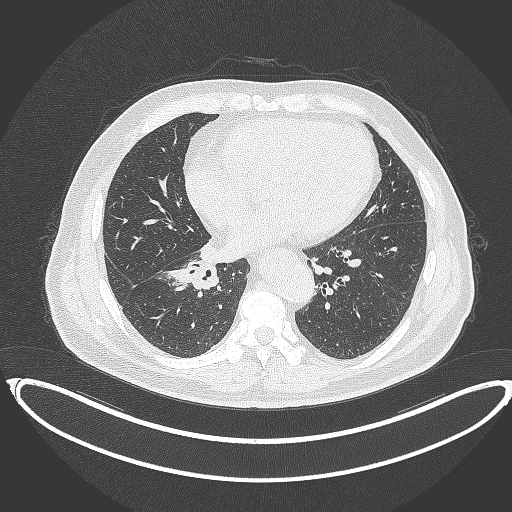
Chest CT, one axial slice. Slice 166 of 387 in the series (ordered by position). Reconstruction kernel B70f. Lung window (W 1500 / L -600 HU). 512 × 512 image matrix. Male patient, age 61 years. From the clinical record (not read from this slice): clinical TNM (as recorded): T1b N1 M0.
Annotated regions visible in this slice (rectangle marked by the reading radiologist):
- lung tumour (recorded histology: squamous cell carcinoma): bounding box [x1, y1, x2, y2] px = [159, 257, 221, 293]